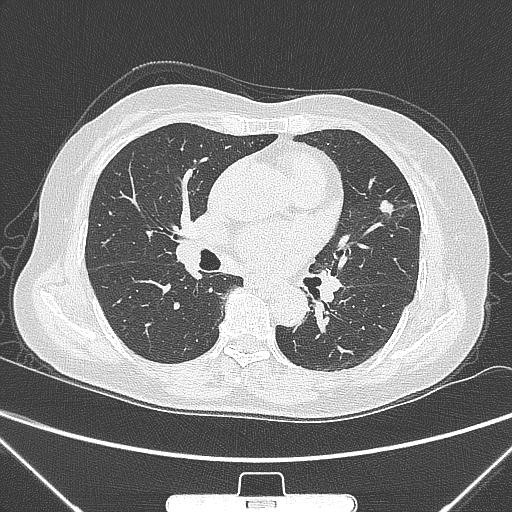
Chest CT, one axial slice. Slice 147 of 300 in the series (ordered by position). 120 kVp. Lung window (W 1500 / L -600 HU). 1 mm slice thickness. 512 × 512 image matrix. Patient: female, 70 years. From the clinical record (not read from this slice): clinical TNM (as recorded): T1b N0 M0.
Annotated regions visible in this slice (bounding box drawn by a radiologist):
- lung tumour (recorded histology: adenocarcinoma): bounding box (x1, y1, x2, y2) in pixels: (377, 198, 408, 230)